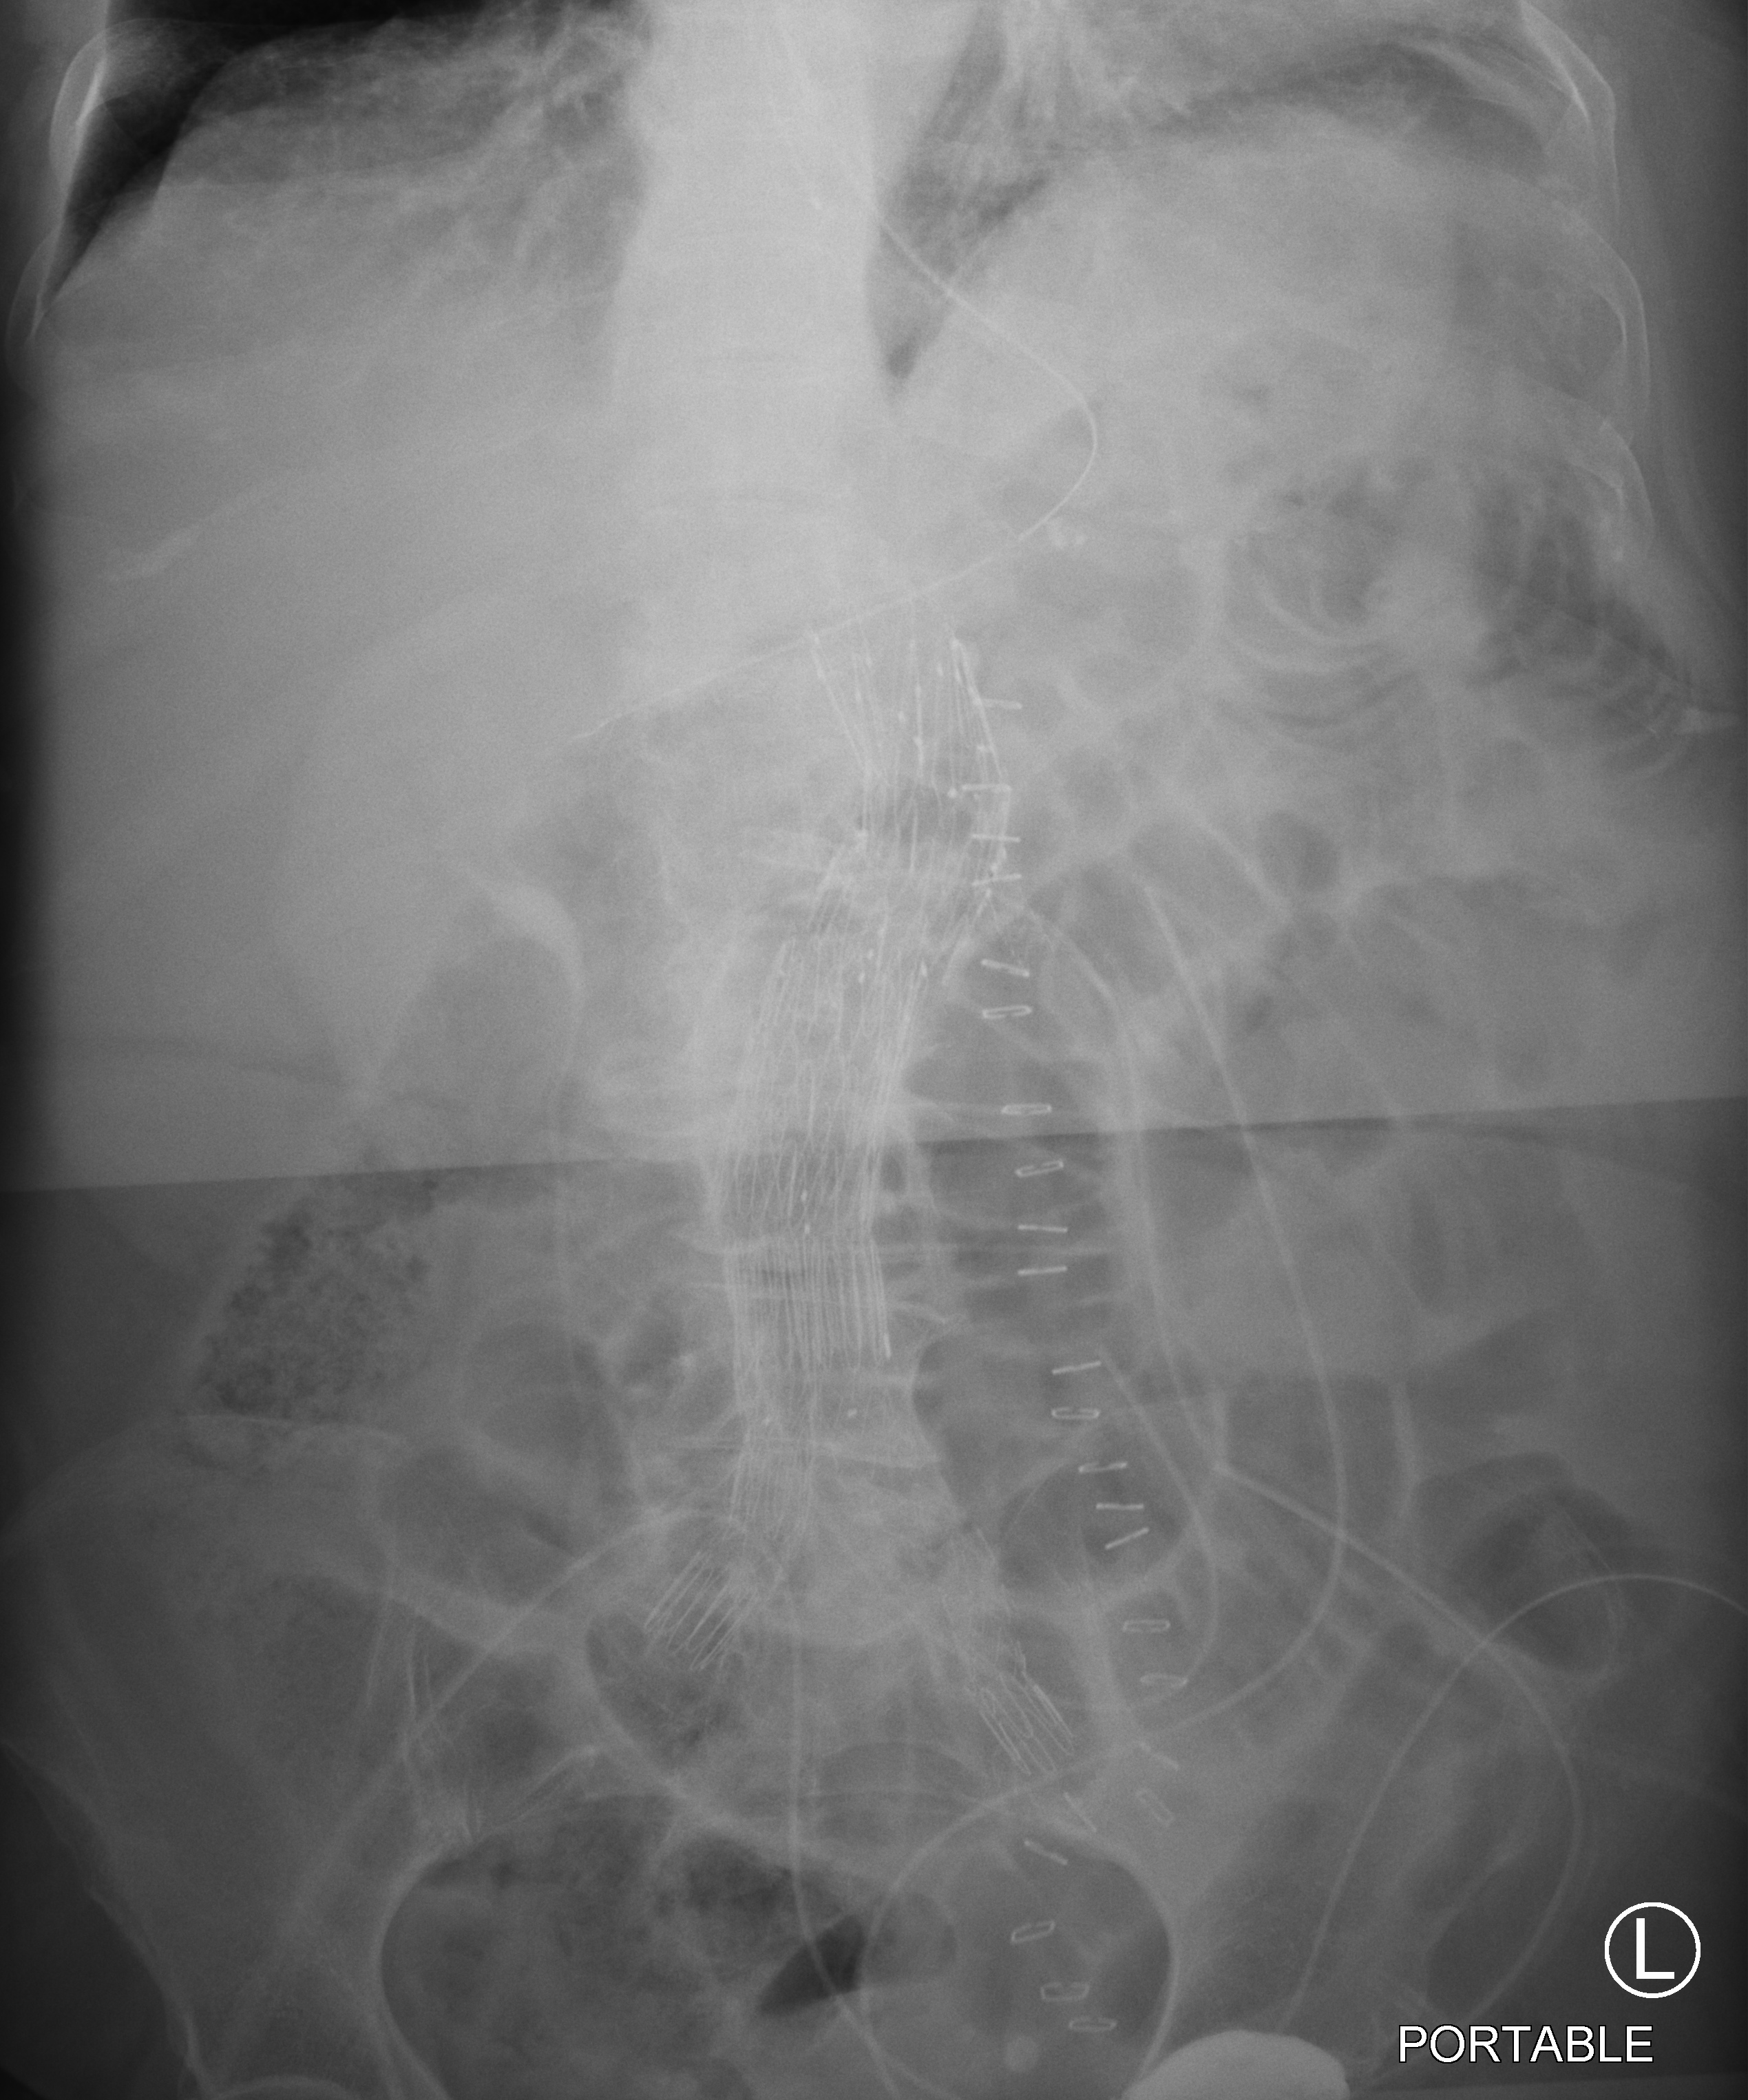
Portable abdomen radiograph; anteroposterior (AP) projection. Patient hospitalised with COVID-19; female, aged 60–74 years.
Admission-level facts for this patient (not findings on this image; timing relative to this image not recorded):
- mechanically ventilated during this hospital stay: no
- admitted to intensive care during this hospital stay: yes
- length of hospital stay: 9 days